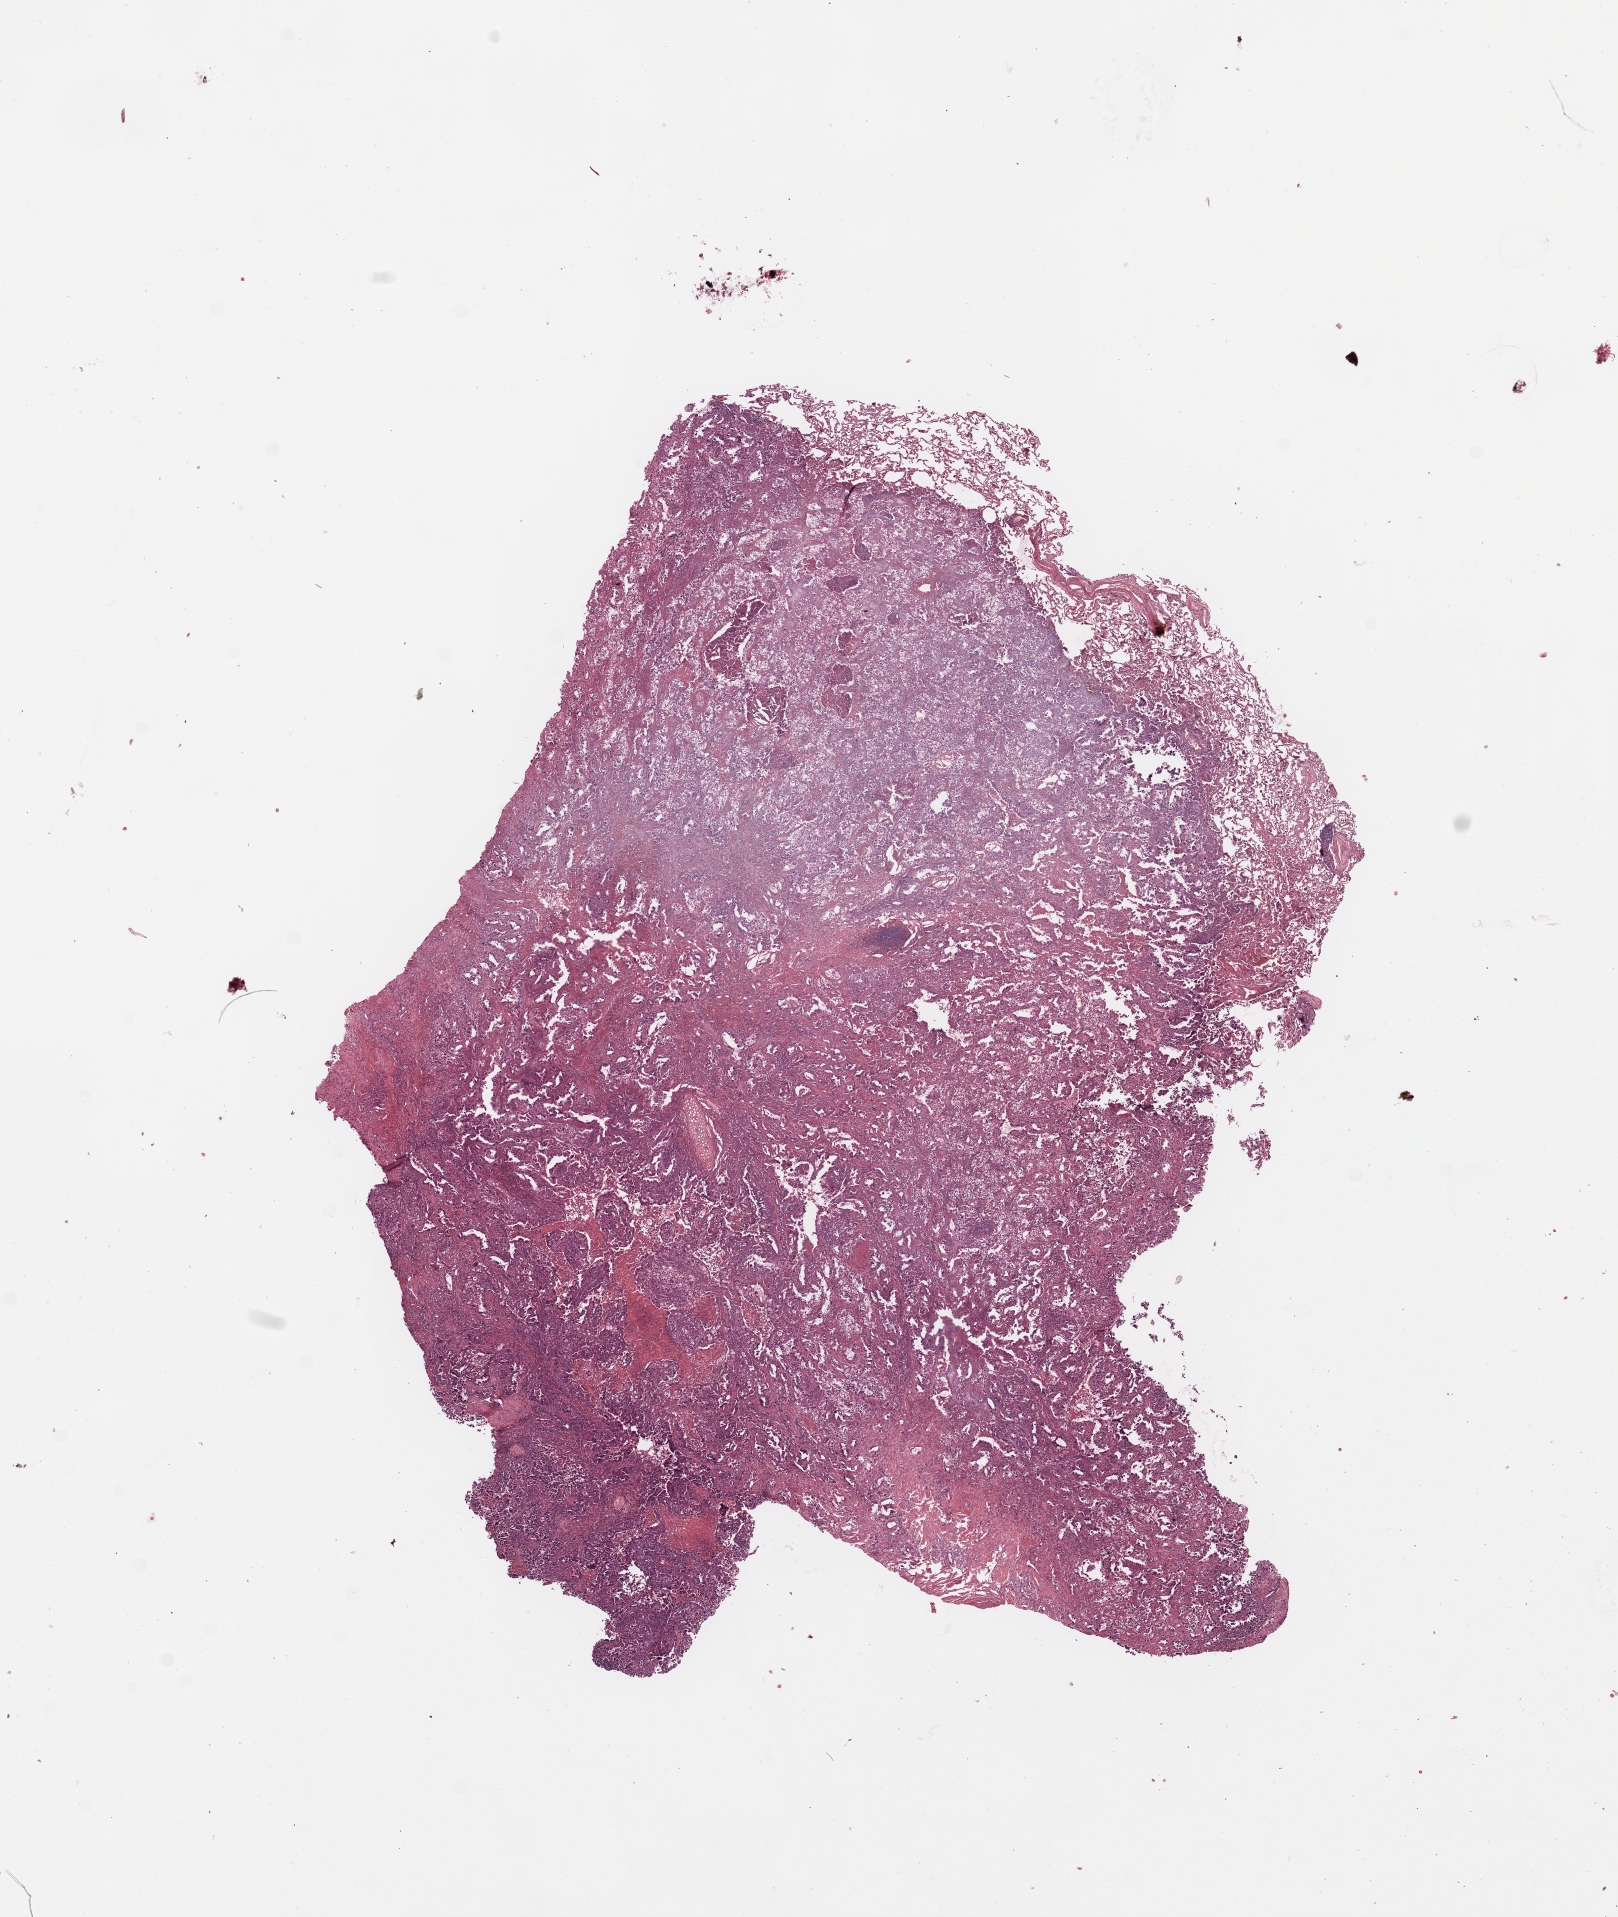
Whole-slide histology image, H&E, shown as a low-resolution overview of the whole scanned area (about 12.8 x 15.2 mm, from a 20x scan). Tumour tissue sample, sampled site: lung. Male, 63 y/o. Histologic grade: G2 (moderately differentiated). Pathologist review of this section (percent, as recorded): tumour nuclei 70%, necrosis 10%.
Primary tumour site (as recorded): left upper lobe. AJCC pathologic stage: IIIA. Diagnosis: Adenocarcinoma, NOS.